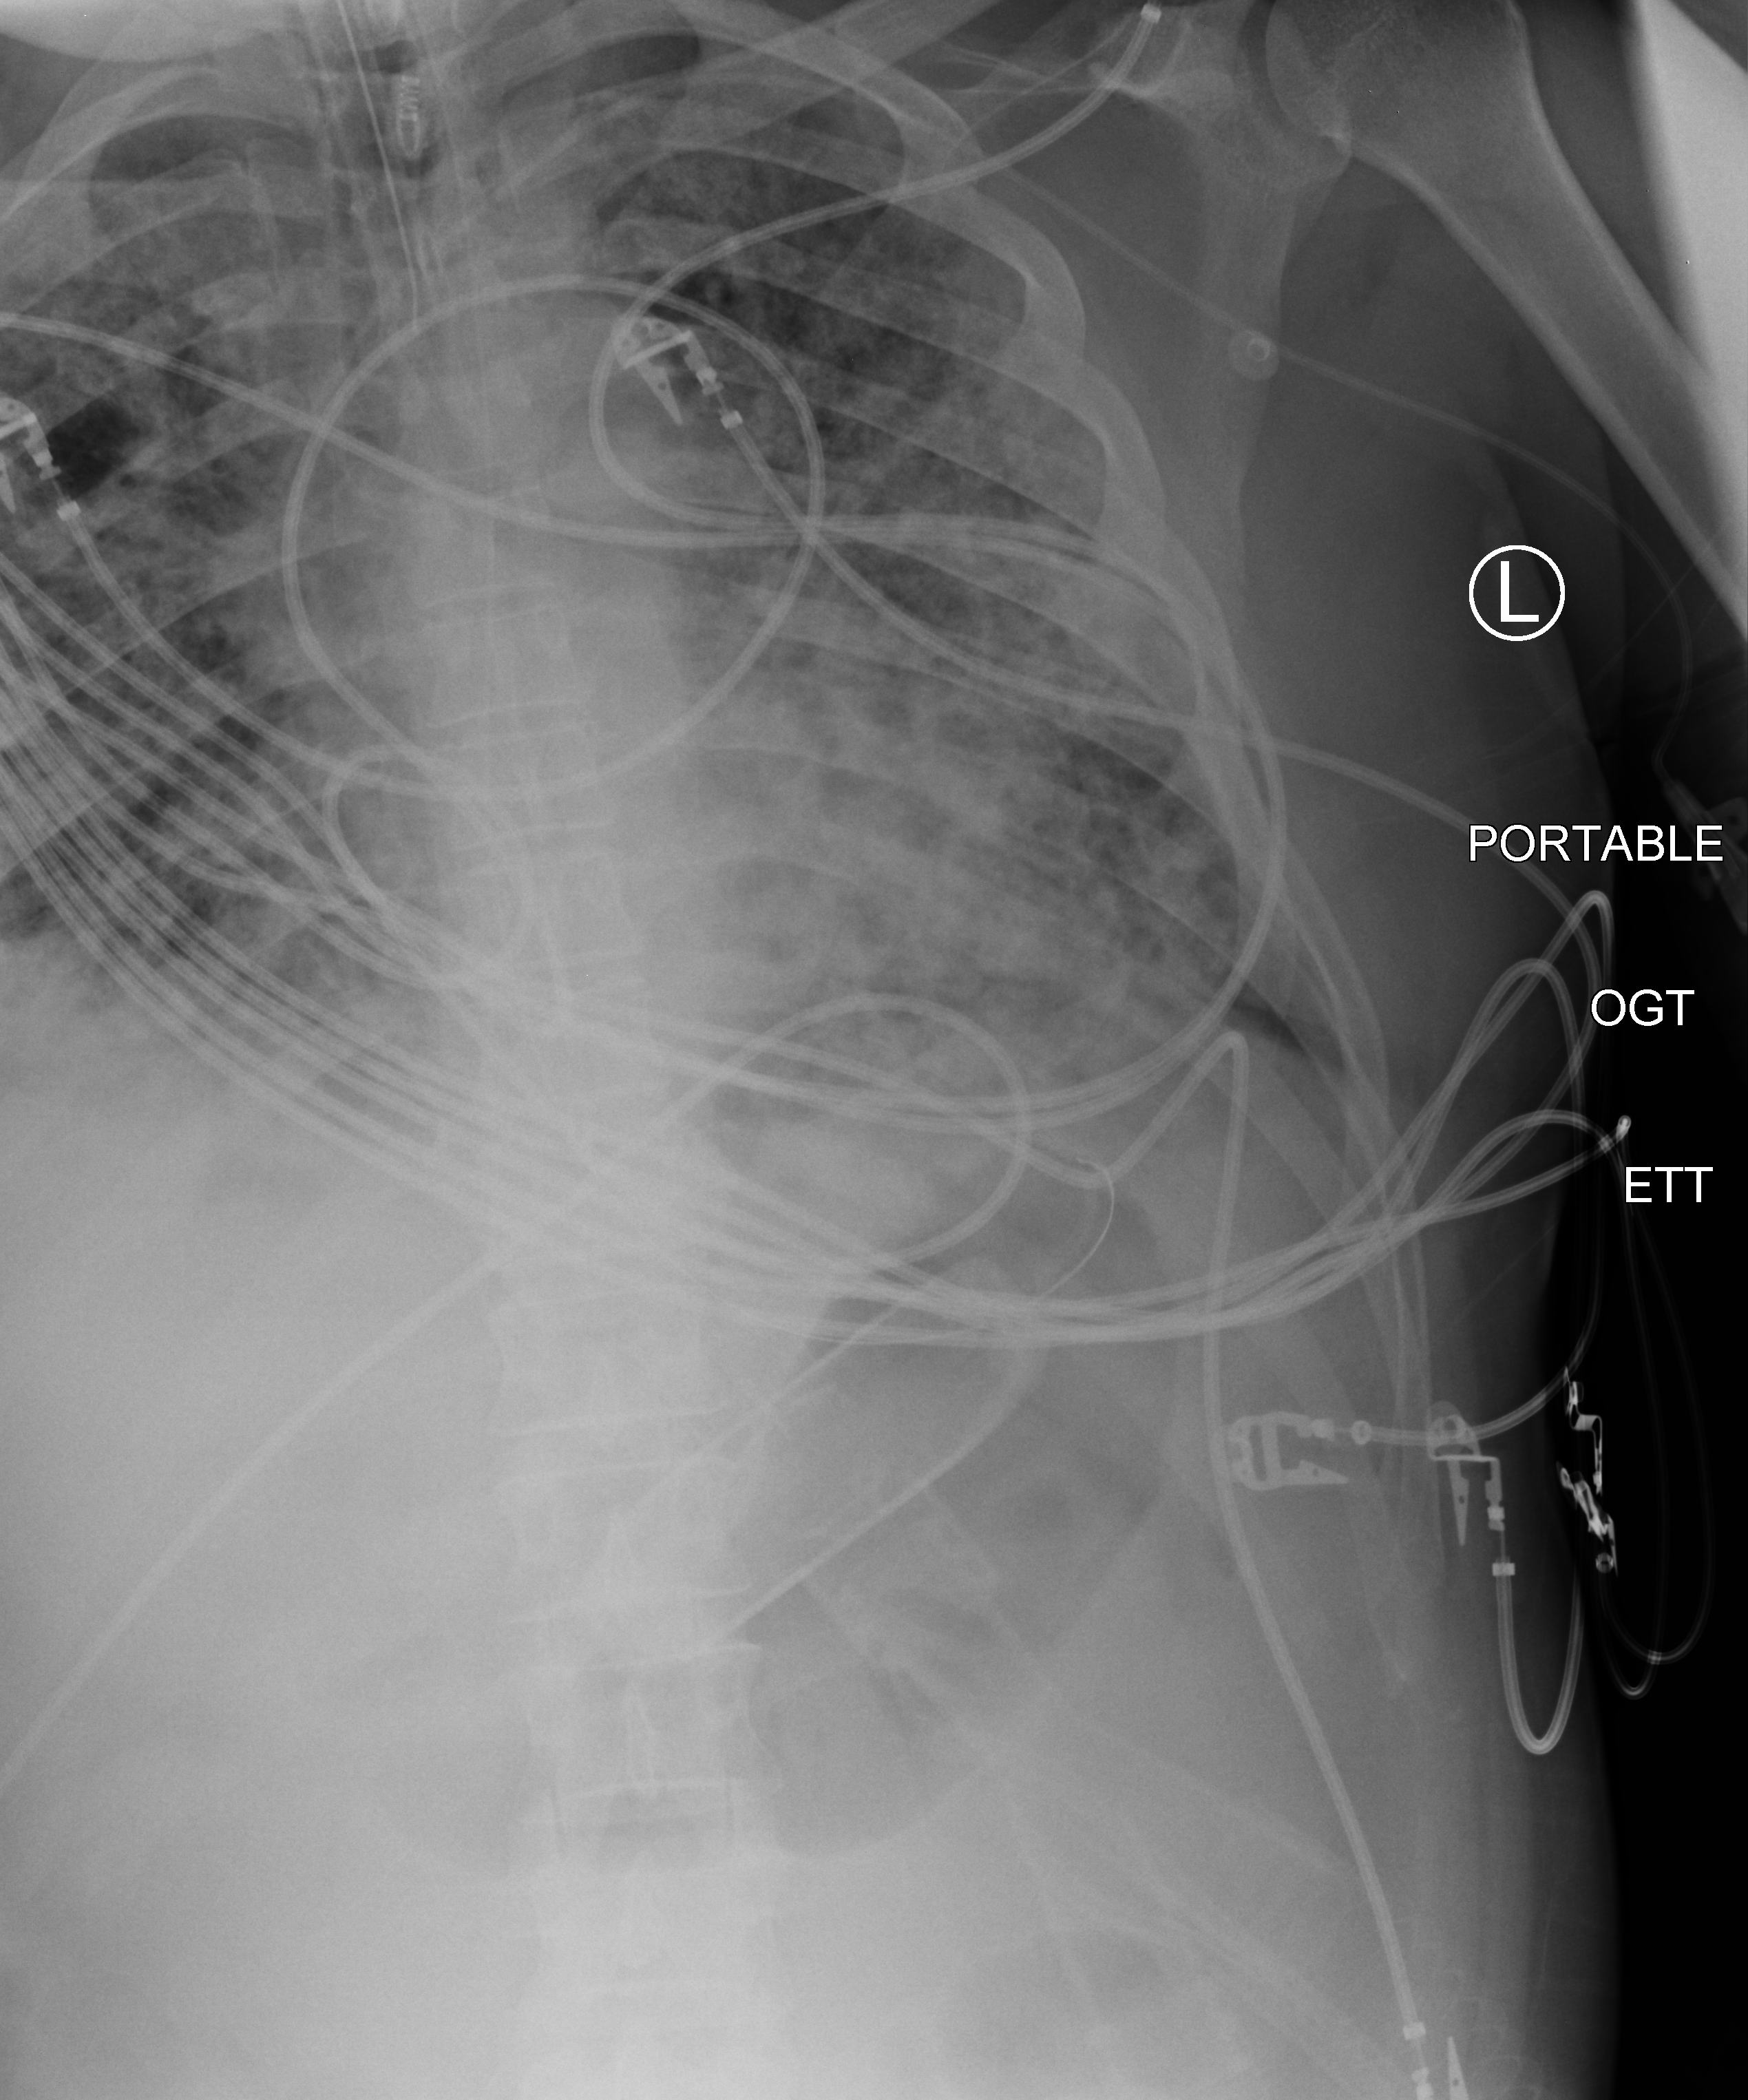
Bedside chest radiograph (computed radiography); anteroposterior (AP) projection. Patient hospitalised with COVID-19; male, aged 18–59 years.
Hospital-stay facts (about this admission, not read from this image; timing relative to this image not recorded): diabetes (admission record): no; mechanically ventilated during this hospital stay: yes; admitted to intensive care during this hospital stay: yes.